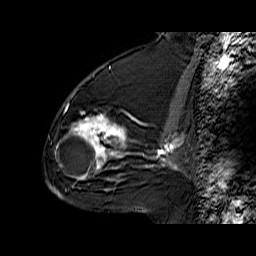
Breast MRI (dynamic contrast-enhanced), one sagittal slice. Slice 36 of 60 in the series (ordered by position). Dynamic contrast-enhanced series, time point 2 of 6 at this slice position (early post-contrast). 1.5 T. TE 6.3 ms, TR 32.9 ms. 256 × 256 image matrix, field of view 200 × 200 mm. Female patient. From the clinical record (not read from this slice): setting: breast cancer imaged before/during neoadjuvant chemotherapy; receptor status: triple-negative.
Annotated regions visible in this slice (semi-automatically segmented with operator editing):
- analysis volume of interest (the breast-tissue region the enhancement analysis was run in; not a lesion): bounding box [x1, y1, x2, y2] px = [55, 76, 127, 170]
- tumour enhancement mask (voxels above the 100 % enhancement threshold inside the analysis volume of interest): [71, 116, 127, 169]